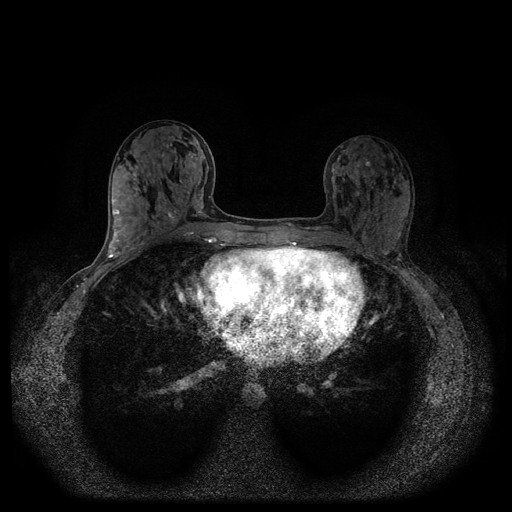
Breast MRI (dynamic contrast-enhanced, multi-phase), one axial slice; slice 43 of 116 in the series (ordered by position); dynamic contrast-enhanced series, time point 2 of 5 at this slice position (early post-contrast); 1.5 T; TE 2.6 ms, TR 5.4 ms; 2 mm slice thickness; 512 × 512 image matrix, field of view 340 × 340 mm. Patient: female, 32 years.
Outlined on this slice (semi-automatic segmentation, software-assisted and operator-edited):
- breast lesion (labelled benign in the annotation): box from (x=352, y=170) to (x=361, y=188) px